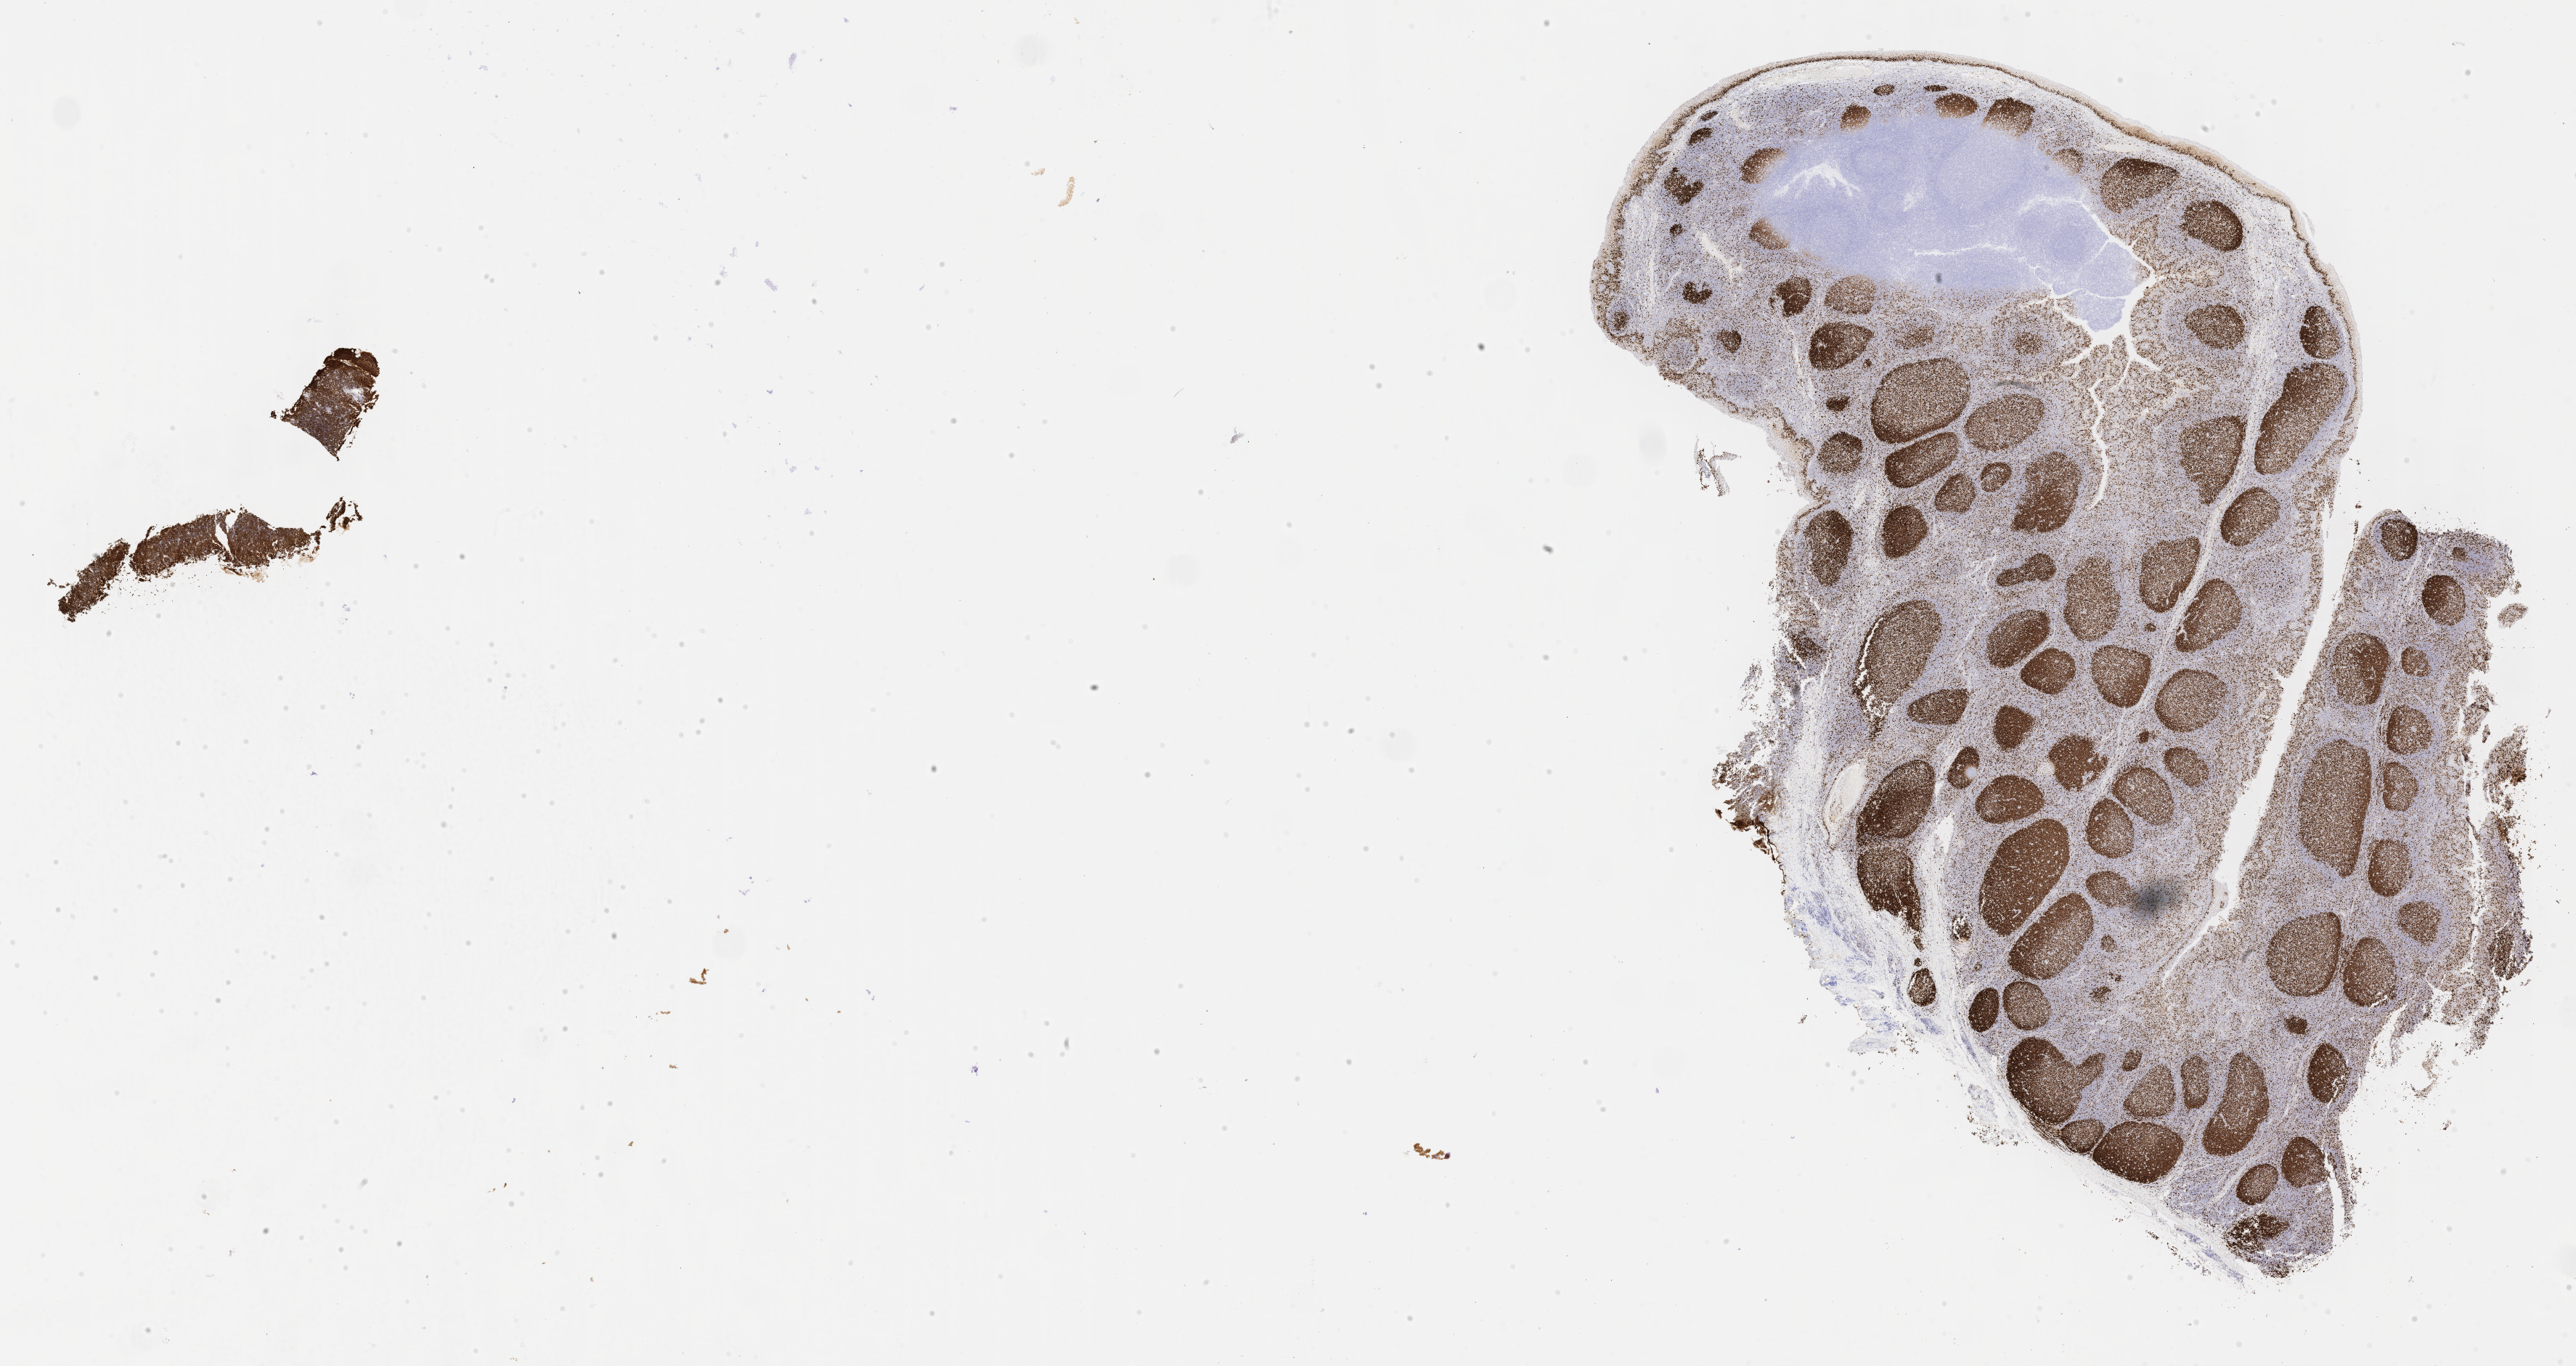
Immunohistochemistry (IHC) whole-slide image stained for Ki-67, low-resolution overview of the scanned area, about 28.7 x 15.2 mm; tumor tissue; anatomic site: cranium. Male, age 6 years at initial diagnosis.
Diagnosis: Burkitt lymphoma, NOS.